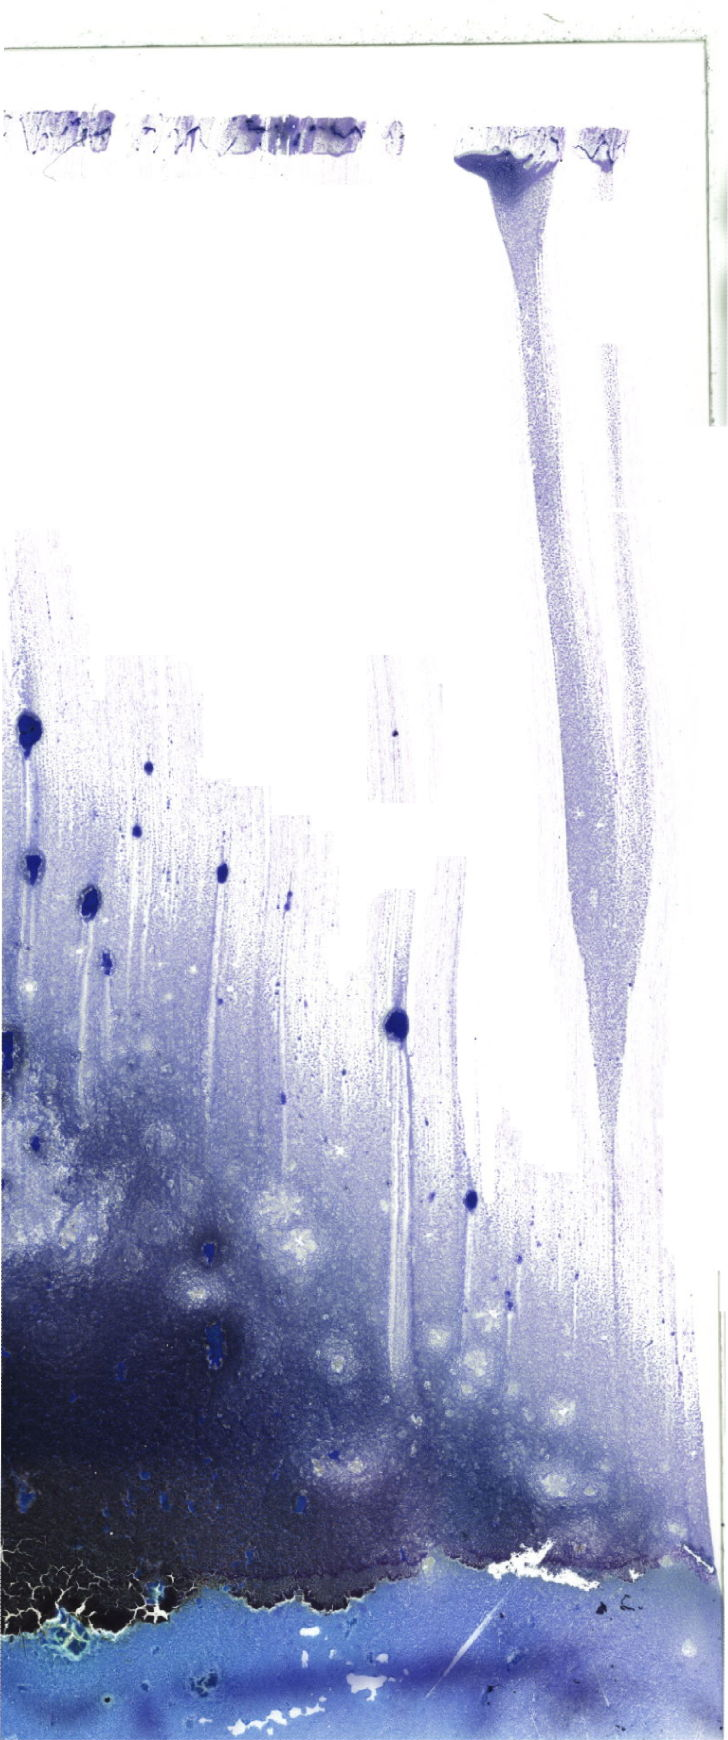
May-Grünwald-Giemsa (MGG)-stained marrow aspirate smear (whole slide) — shown as a low-resolution overview of the whole scanned area (about 20.6 x 49.3 mm). Female patient.
* diagnosis: Chronic Phase Chronic Myeloid Leukemia, BCR-ABL1 Positive